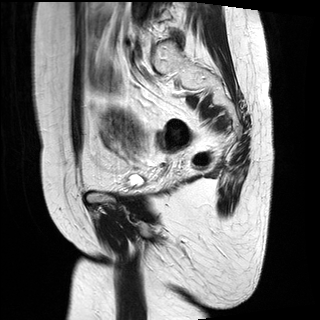
Pelvic MRI for cervical cancer, one sagittal slice. T2-weighted. 1.5 T. TE 89 ms, TR 2740 ms. 4 mm slice thickness. 320 × 320 image matrix. Patient: female, 49 years.
Structures marked on this image (outlined manually by an expert reader):
- uterus and cervix: bounding box (x1, y1, x2, y2) in pixels: (101, 105, 146, 158)